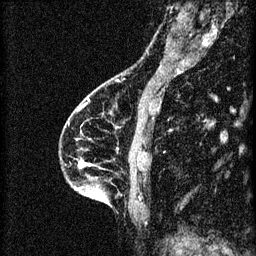
Breast MRI (dynamic contrast-enhanced), one sagittal slice. 3 images stored at this slice position (order not interpretable as contrast timing). 1.5 T. TE 4.2 ms, TR 8.2 ms. 2 mm slice thickness. 256 × 256 image matrix, field of view 180 × 180 mm. Patient: female, 46 years.
Annotated regions visible in this slice (semi-automatic segmentation, software-assisted and operator-edited):
- analysis volume of interest (the breast-tissue region the enhancement analysis was run in; not a lesion): bounding box <60,114,148,209> (left, top, right, bottom; pixels)
- tumour enhancement mask (voxels above the 70 % enhancement threshold inside the analysis volume of interest): <79,160,92,169>